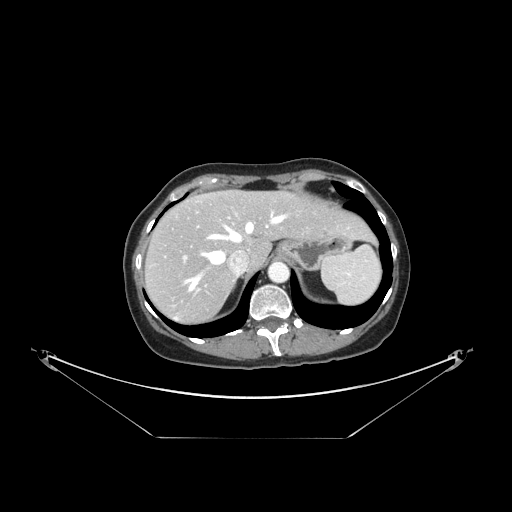
Contrast-enhanced abdominal CT, one axial slice. Reconstruction kernel STANDARD. Intravenous contrast given. Soft-tissue window (W 400 / L 40 HU). 2.5 mm slice thickness. 512 × 512 image matrix. Female patient, age 73 years. Case-level facts recorded for this patient, not image findings: diagnosis: colorectal cancer liver metastases, imaged before liver resection; multiple liver metastases: no.
Structures marked on this image (expert manual segmentation):
- hepatic veins: box from (x=185, y=211) to (x=288, y=291) px
- liver: (x=147, y=191)–(x=372, y=321)
- planned liver remnant (the part of the liver to remain after resection): (x=171, y=191)–(x=371, y=266)
- portal vein (with intrahepatic branches): (x=183, y=256)–(x=187, y=260)